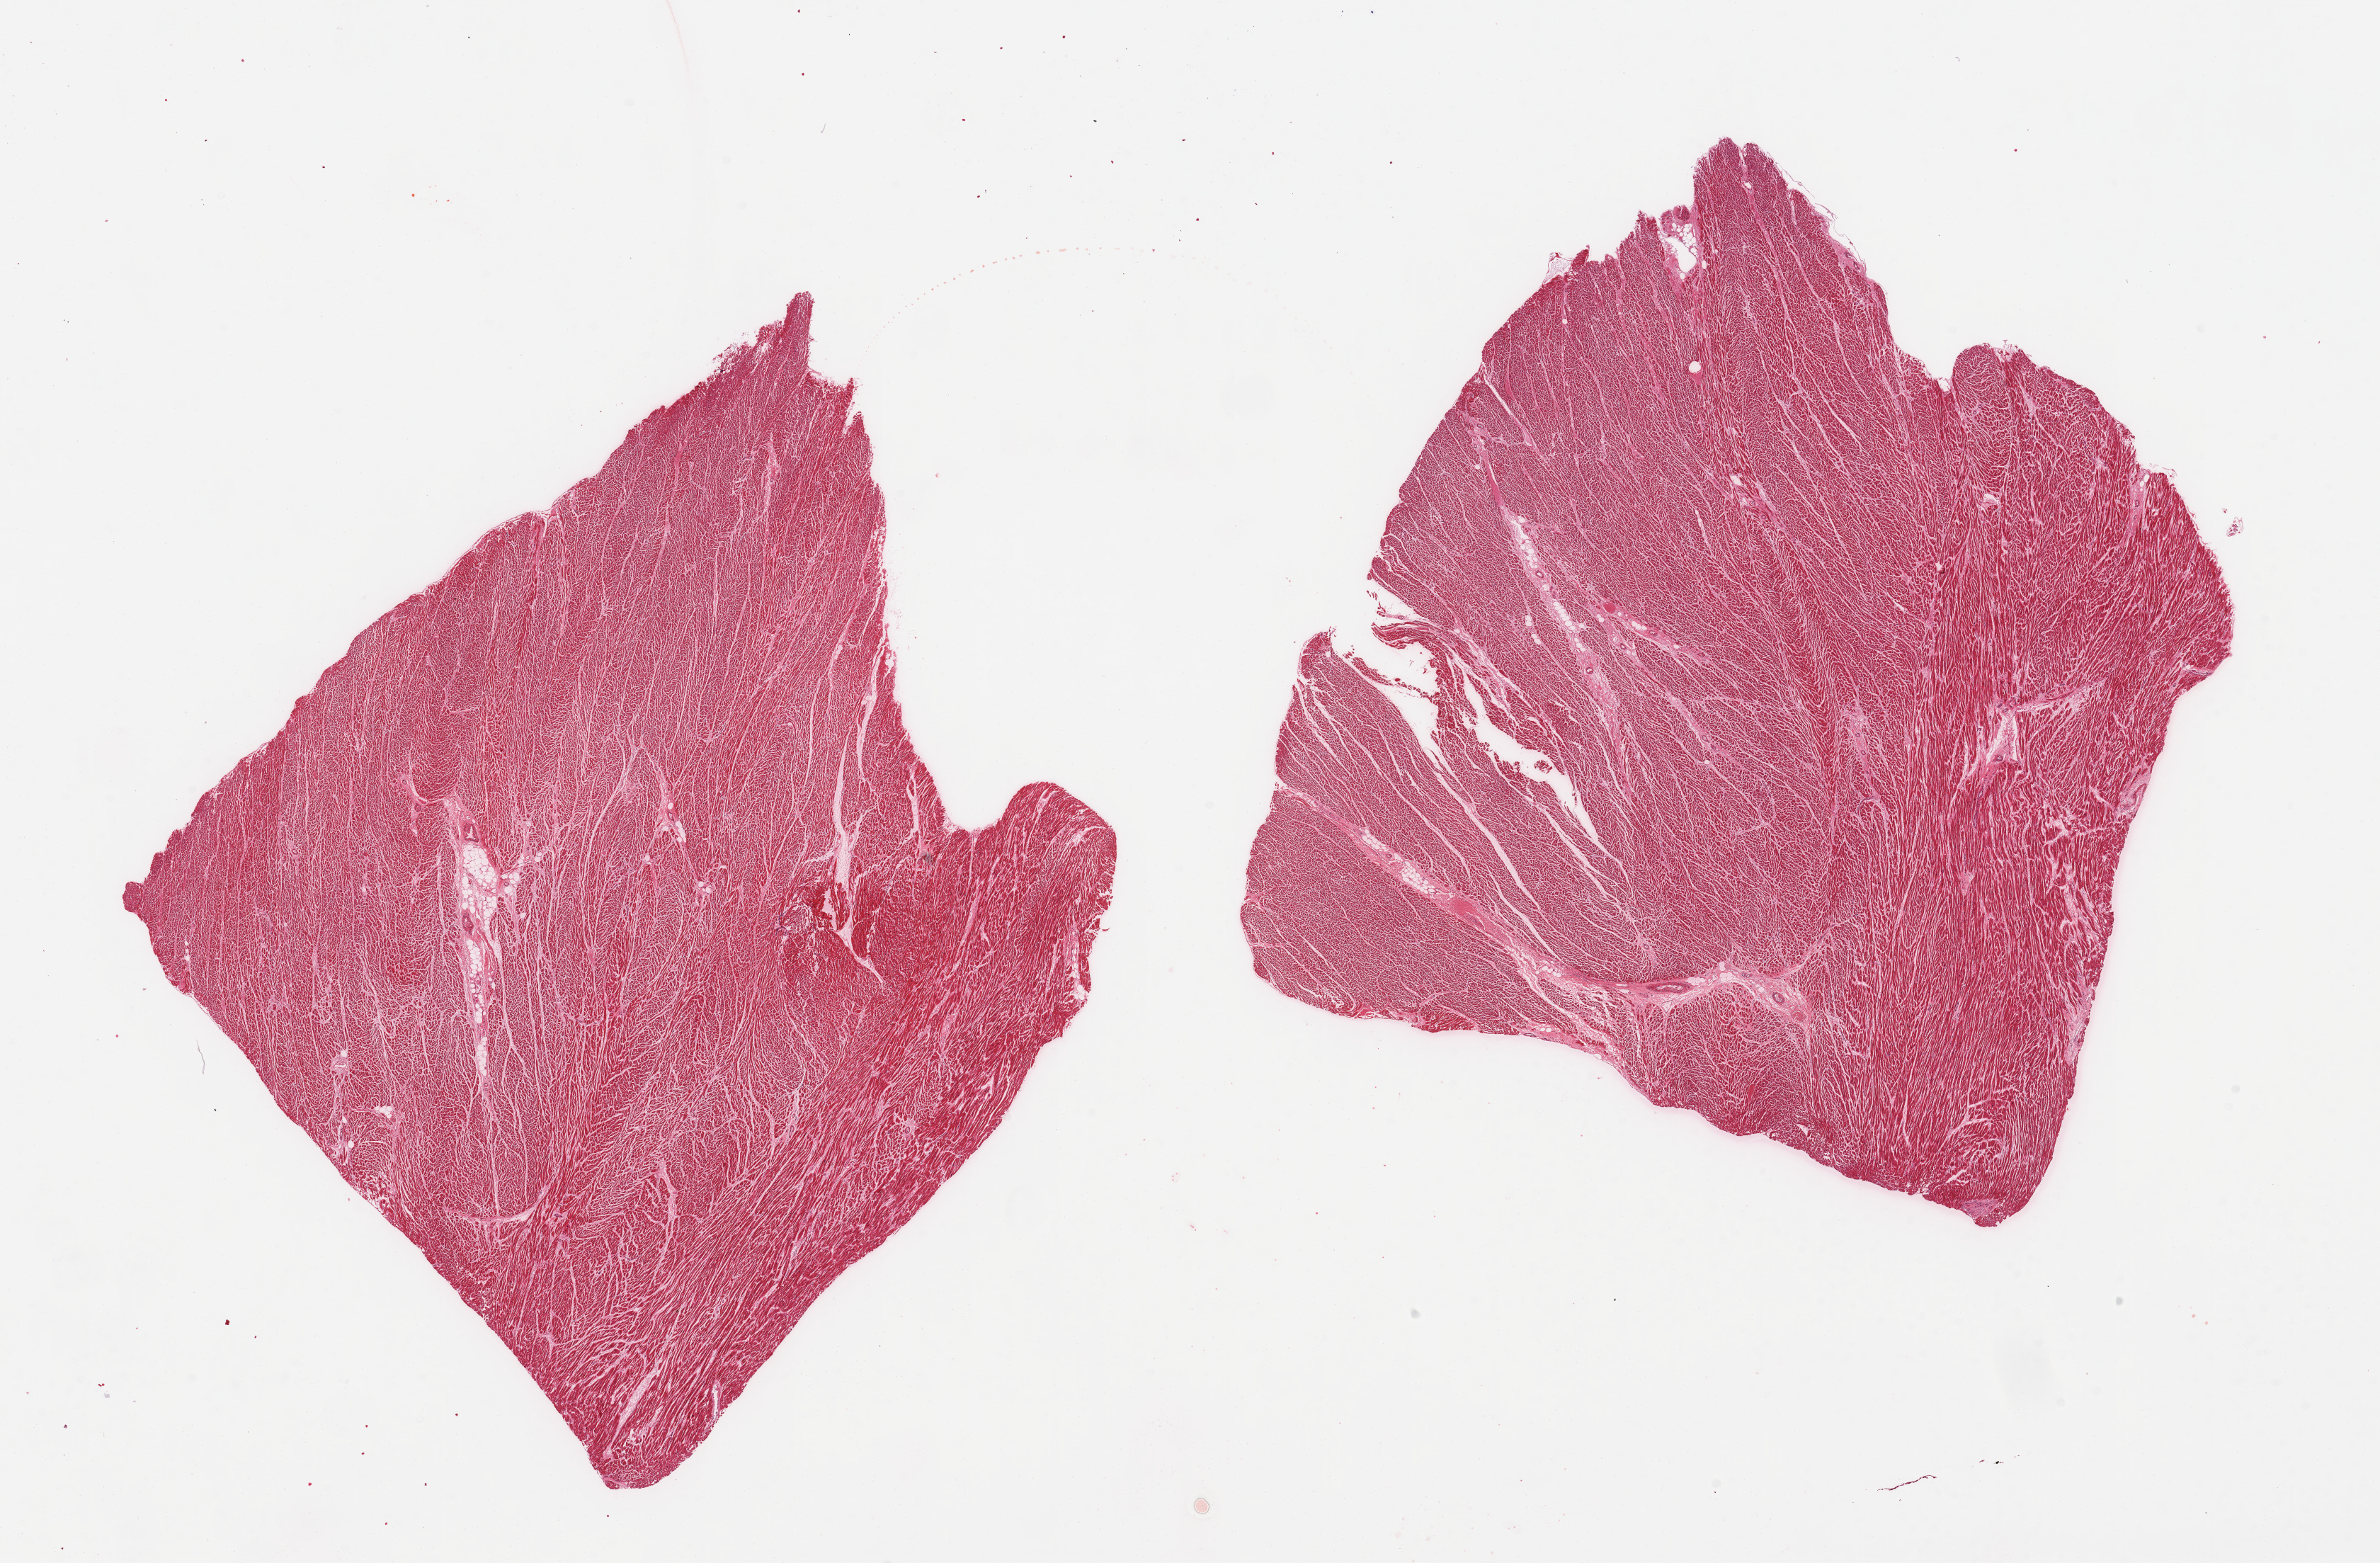
Haematoxylin and eosin whole-slide image, brightfield, shown as a low-resolution overview of the whole scanned area (about 26.6 x 17.5 mm, acquisition: 20x scan), PAXgene-fixed paraffin-embedded (PFPE) section, target tissue: heart, donor tissue sample. Donor: male.
• review note (as recorded): 2 pieces; focal hemorrhage